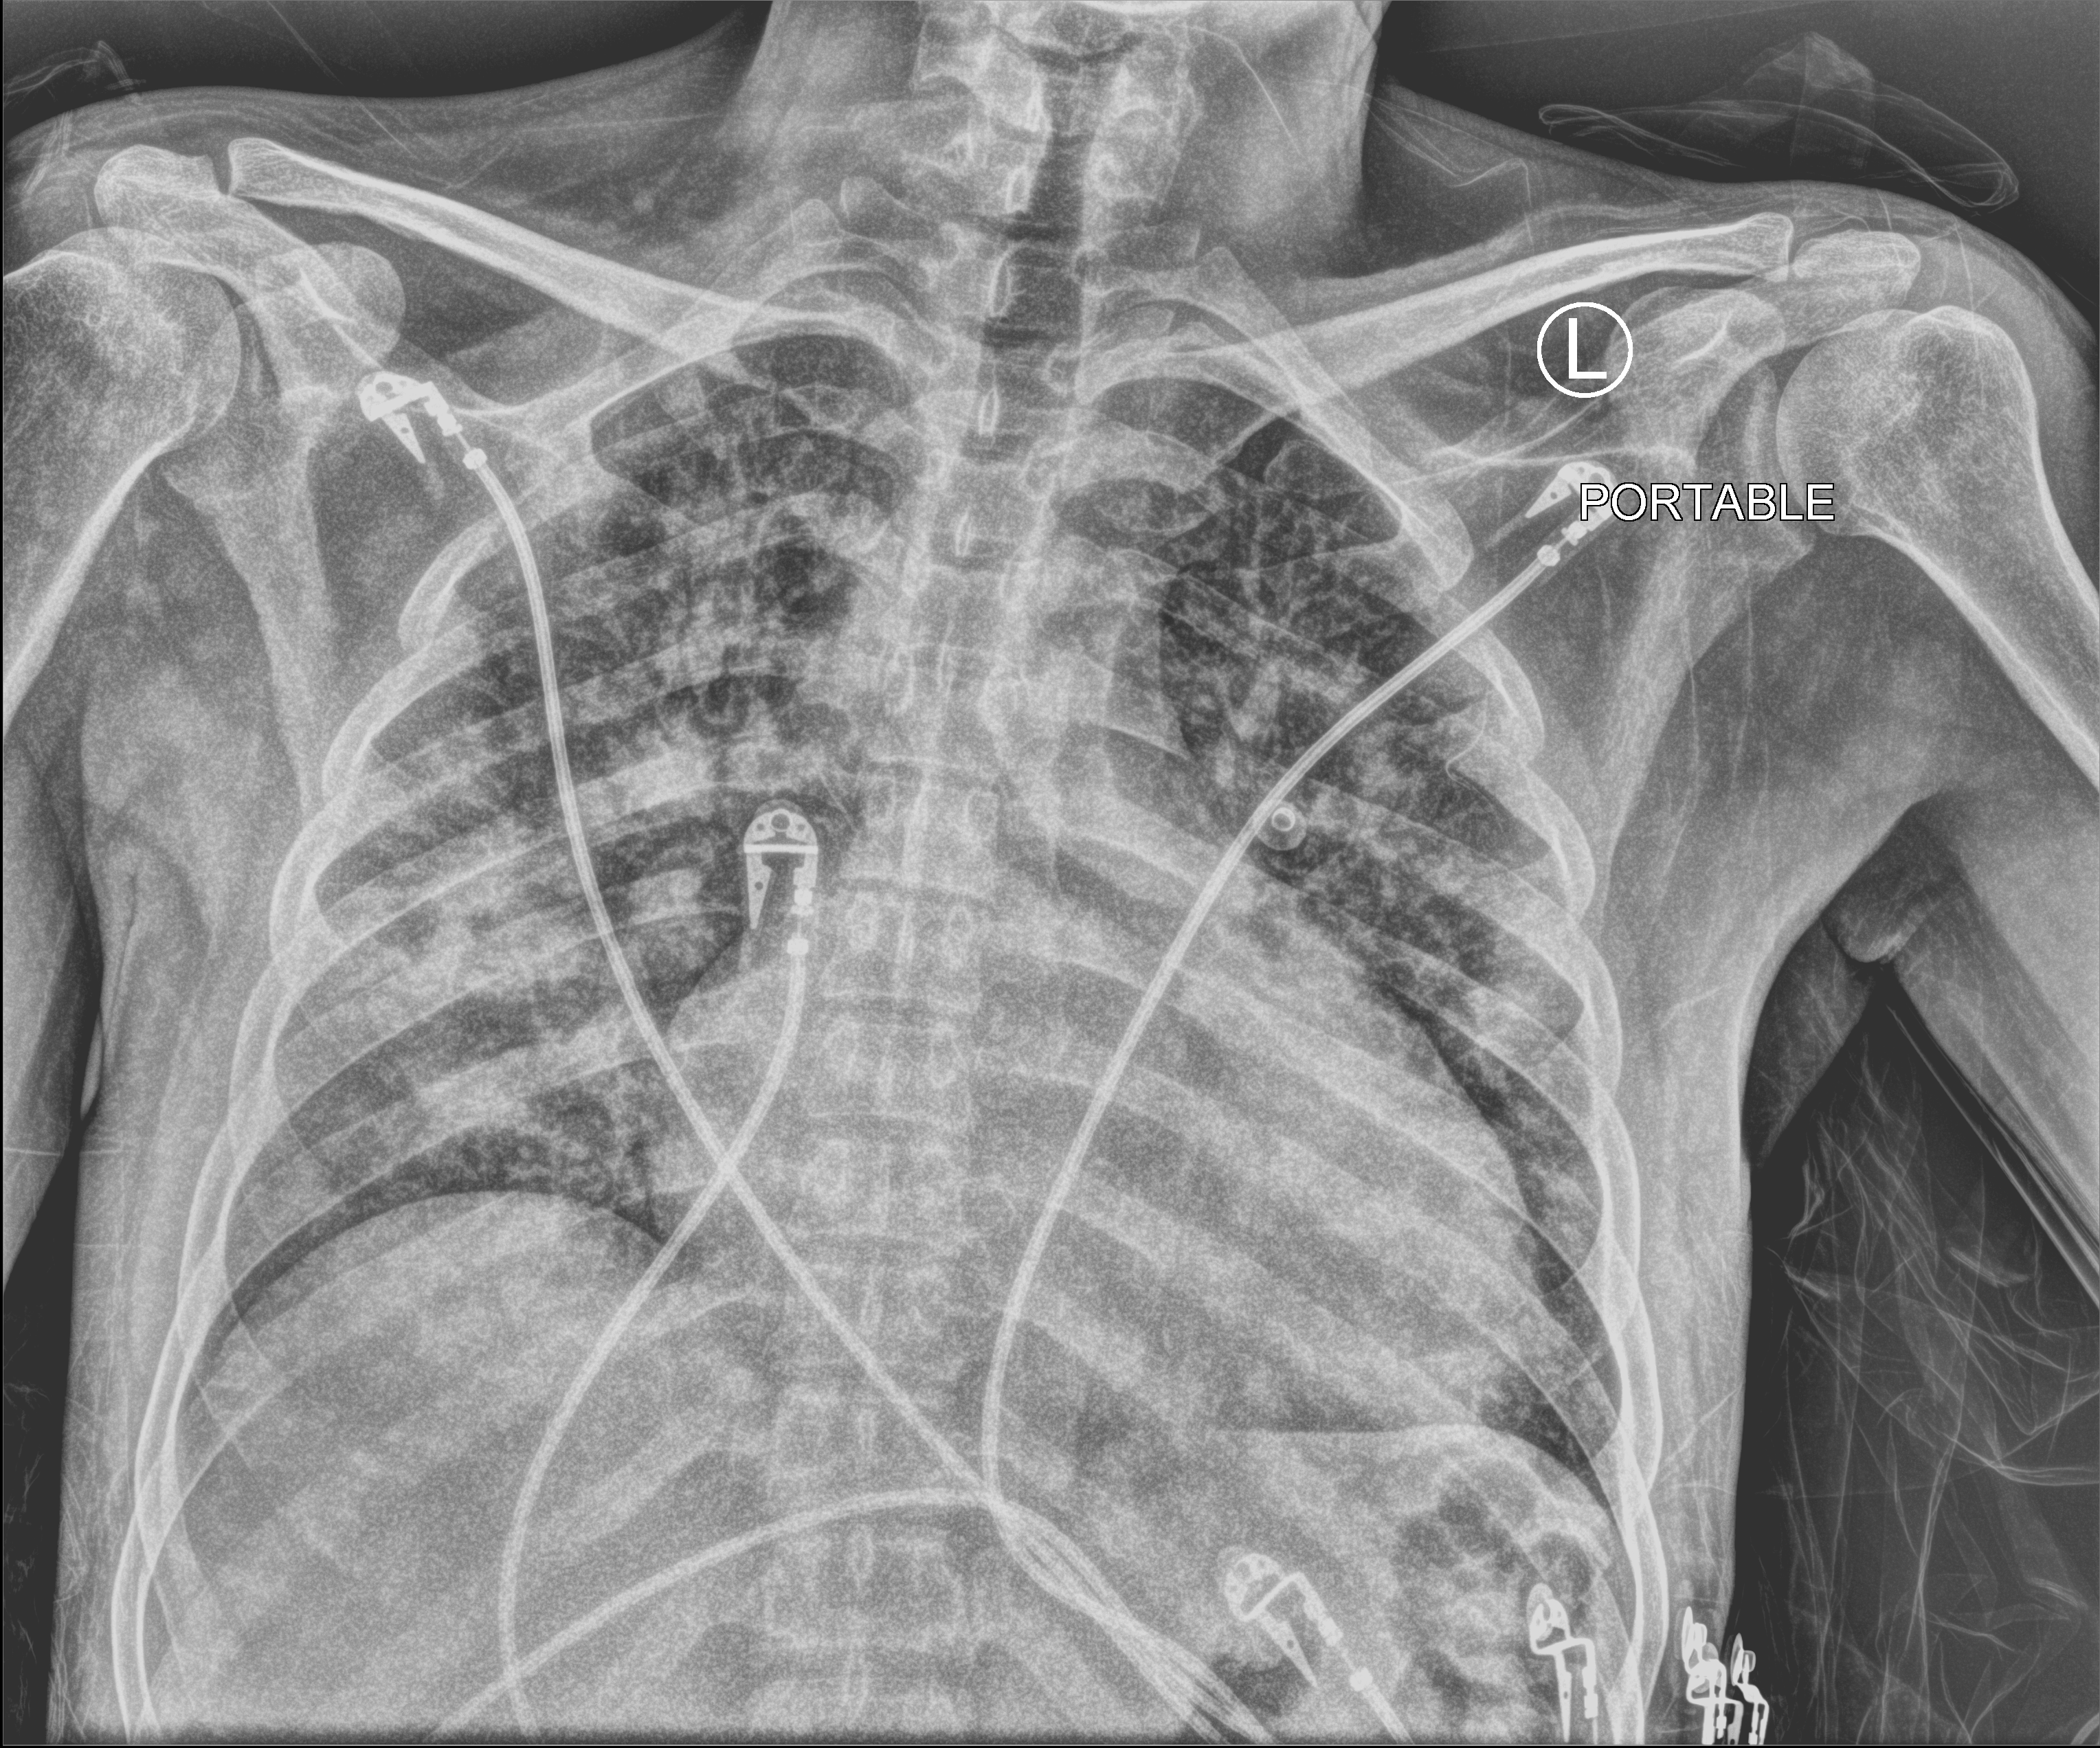
Bedside chest radiograph (computed radiography); anteroposterior (AP) projection. Patient hospitalised with COVID-19; male, aged 18–59 years.
From the hospital-stay record, not from the radiograph (when in the stay this image was taken is not recorded): other chronic lung disease (admission record): no; chronic kidney disease (admission record): yes.